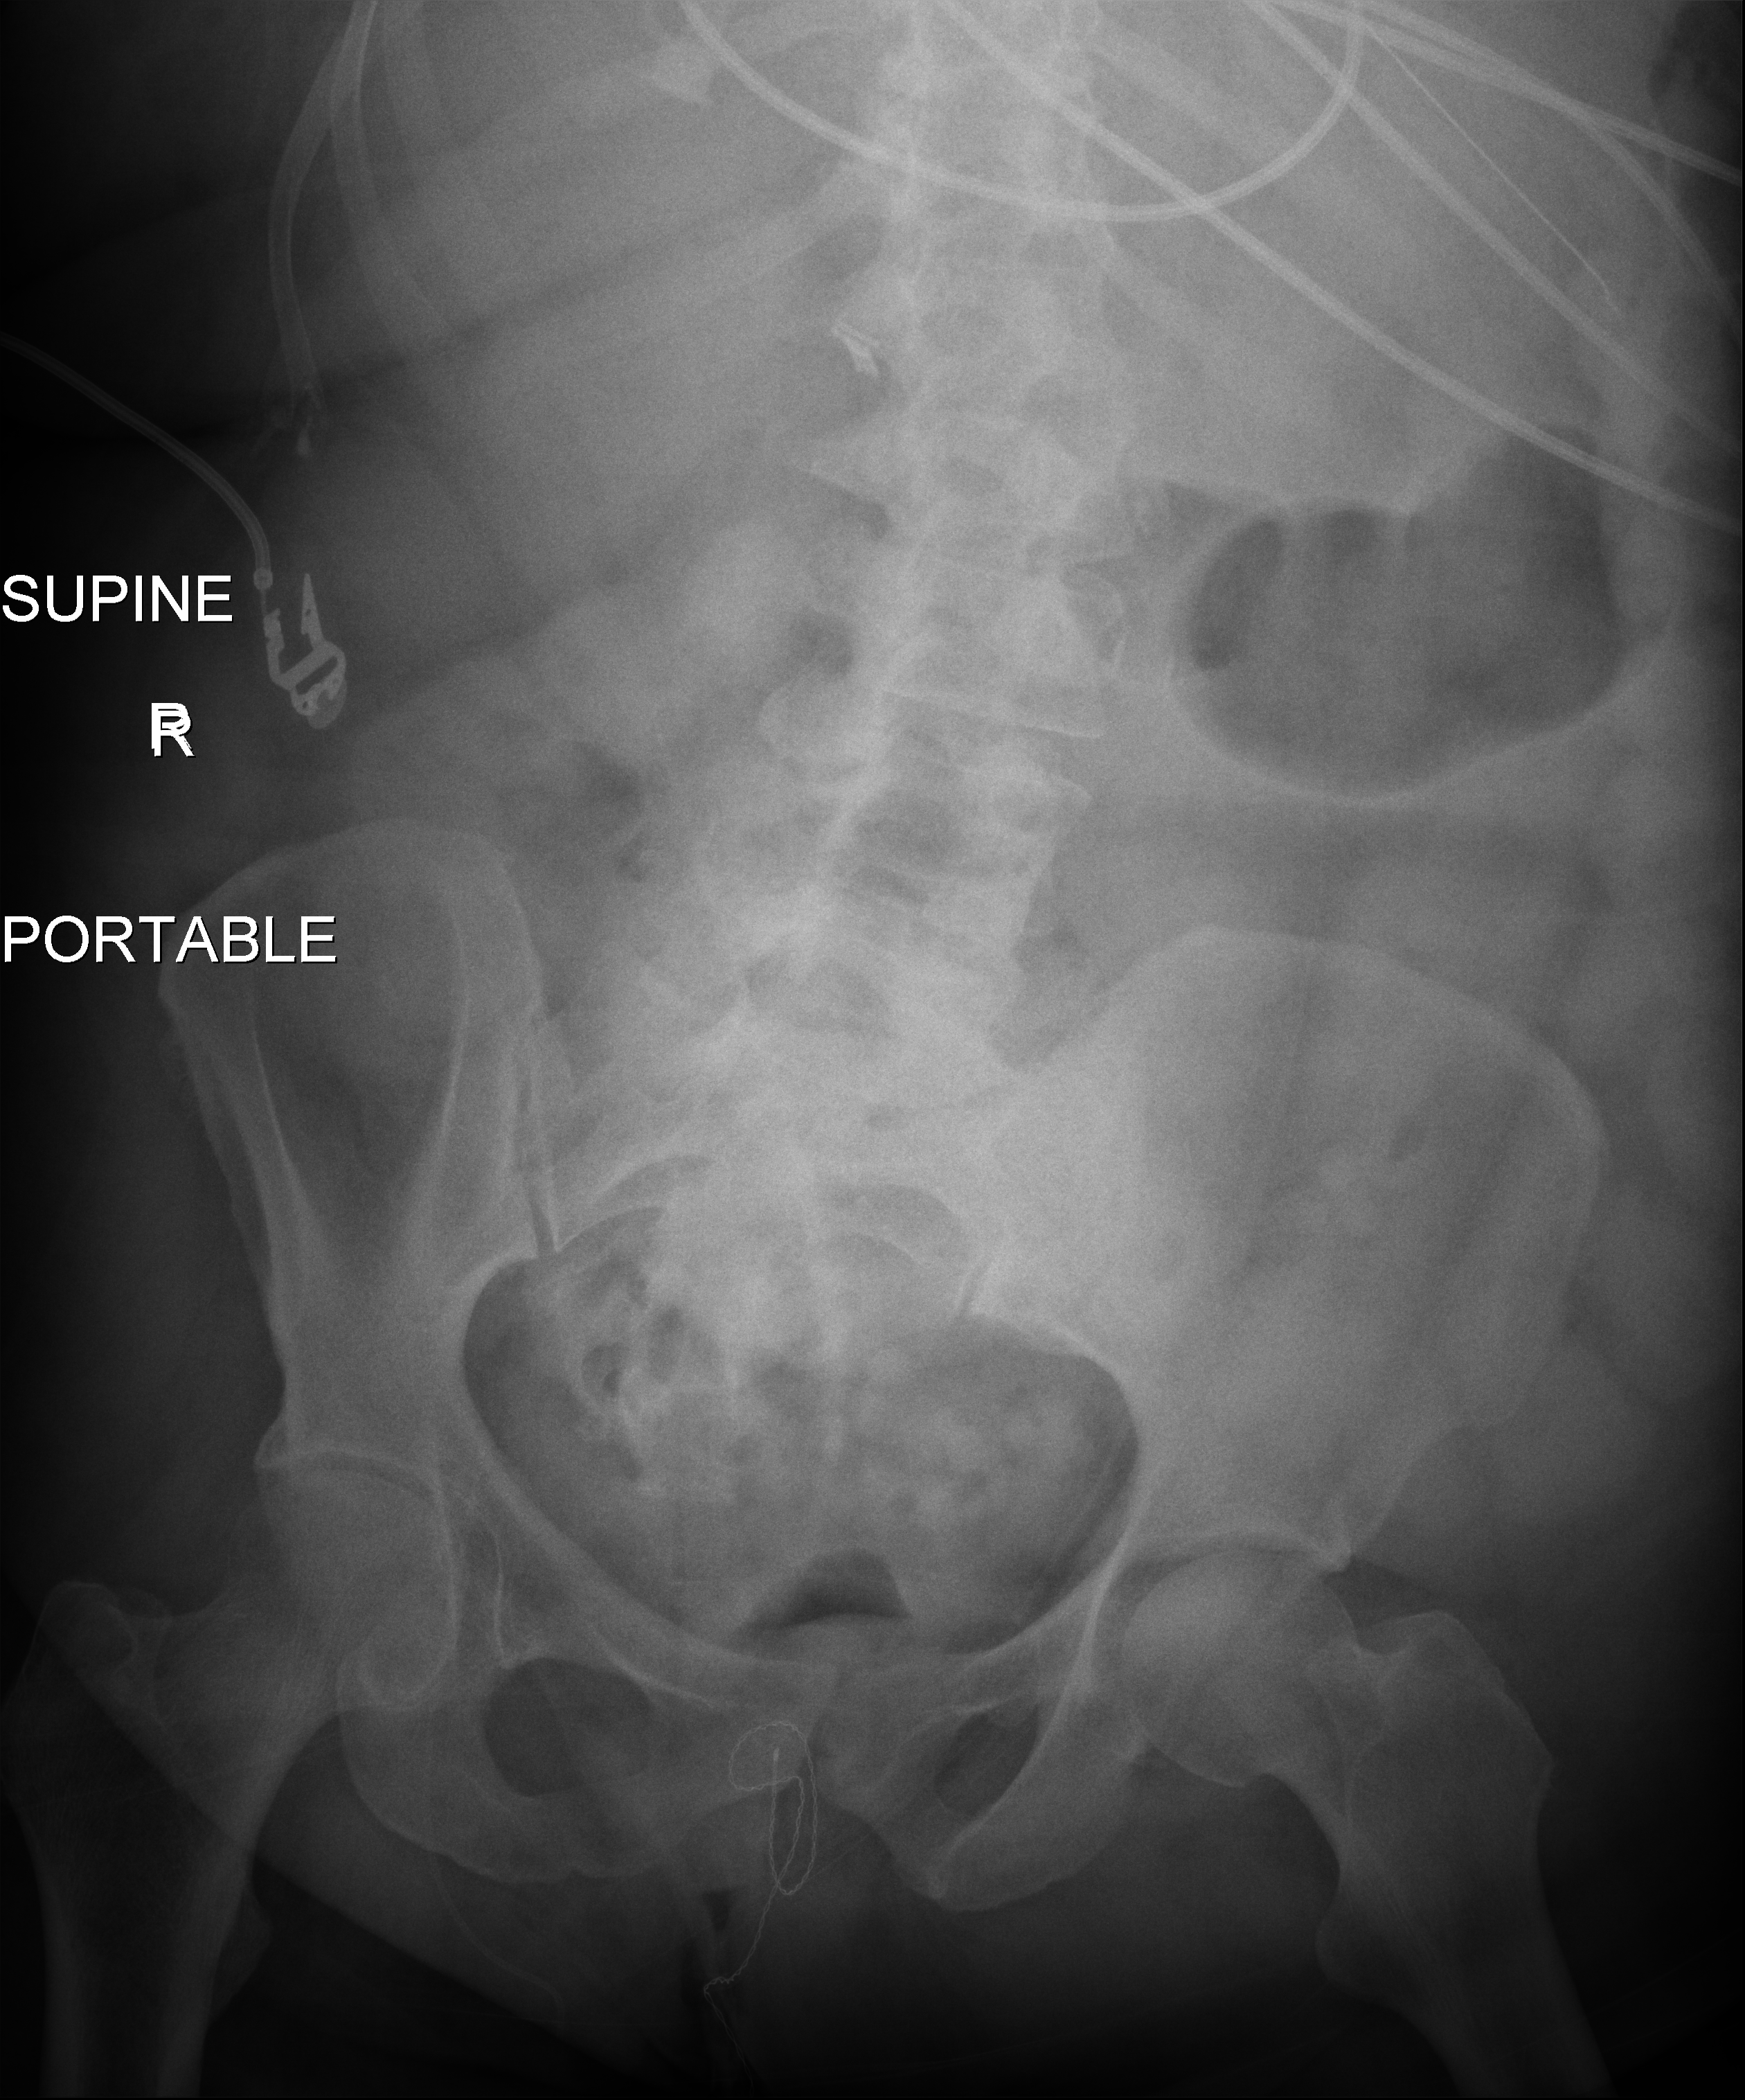
Portable abdomen radiograph. Patient hospitalised with COVID-19; female, aged 60–74 years.
Admission-level facts for this patient (not findings on this image; timing relative to this image not recorded): mechanically ventilated during this hospital stay: yes.